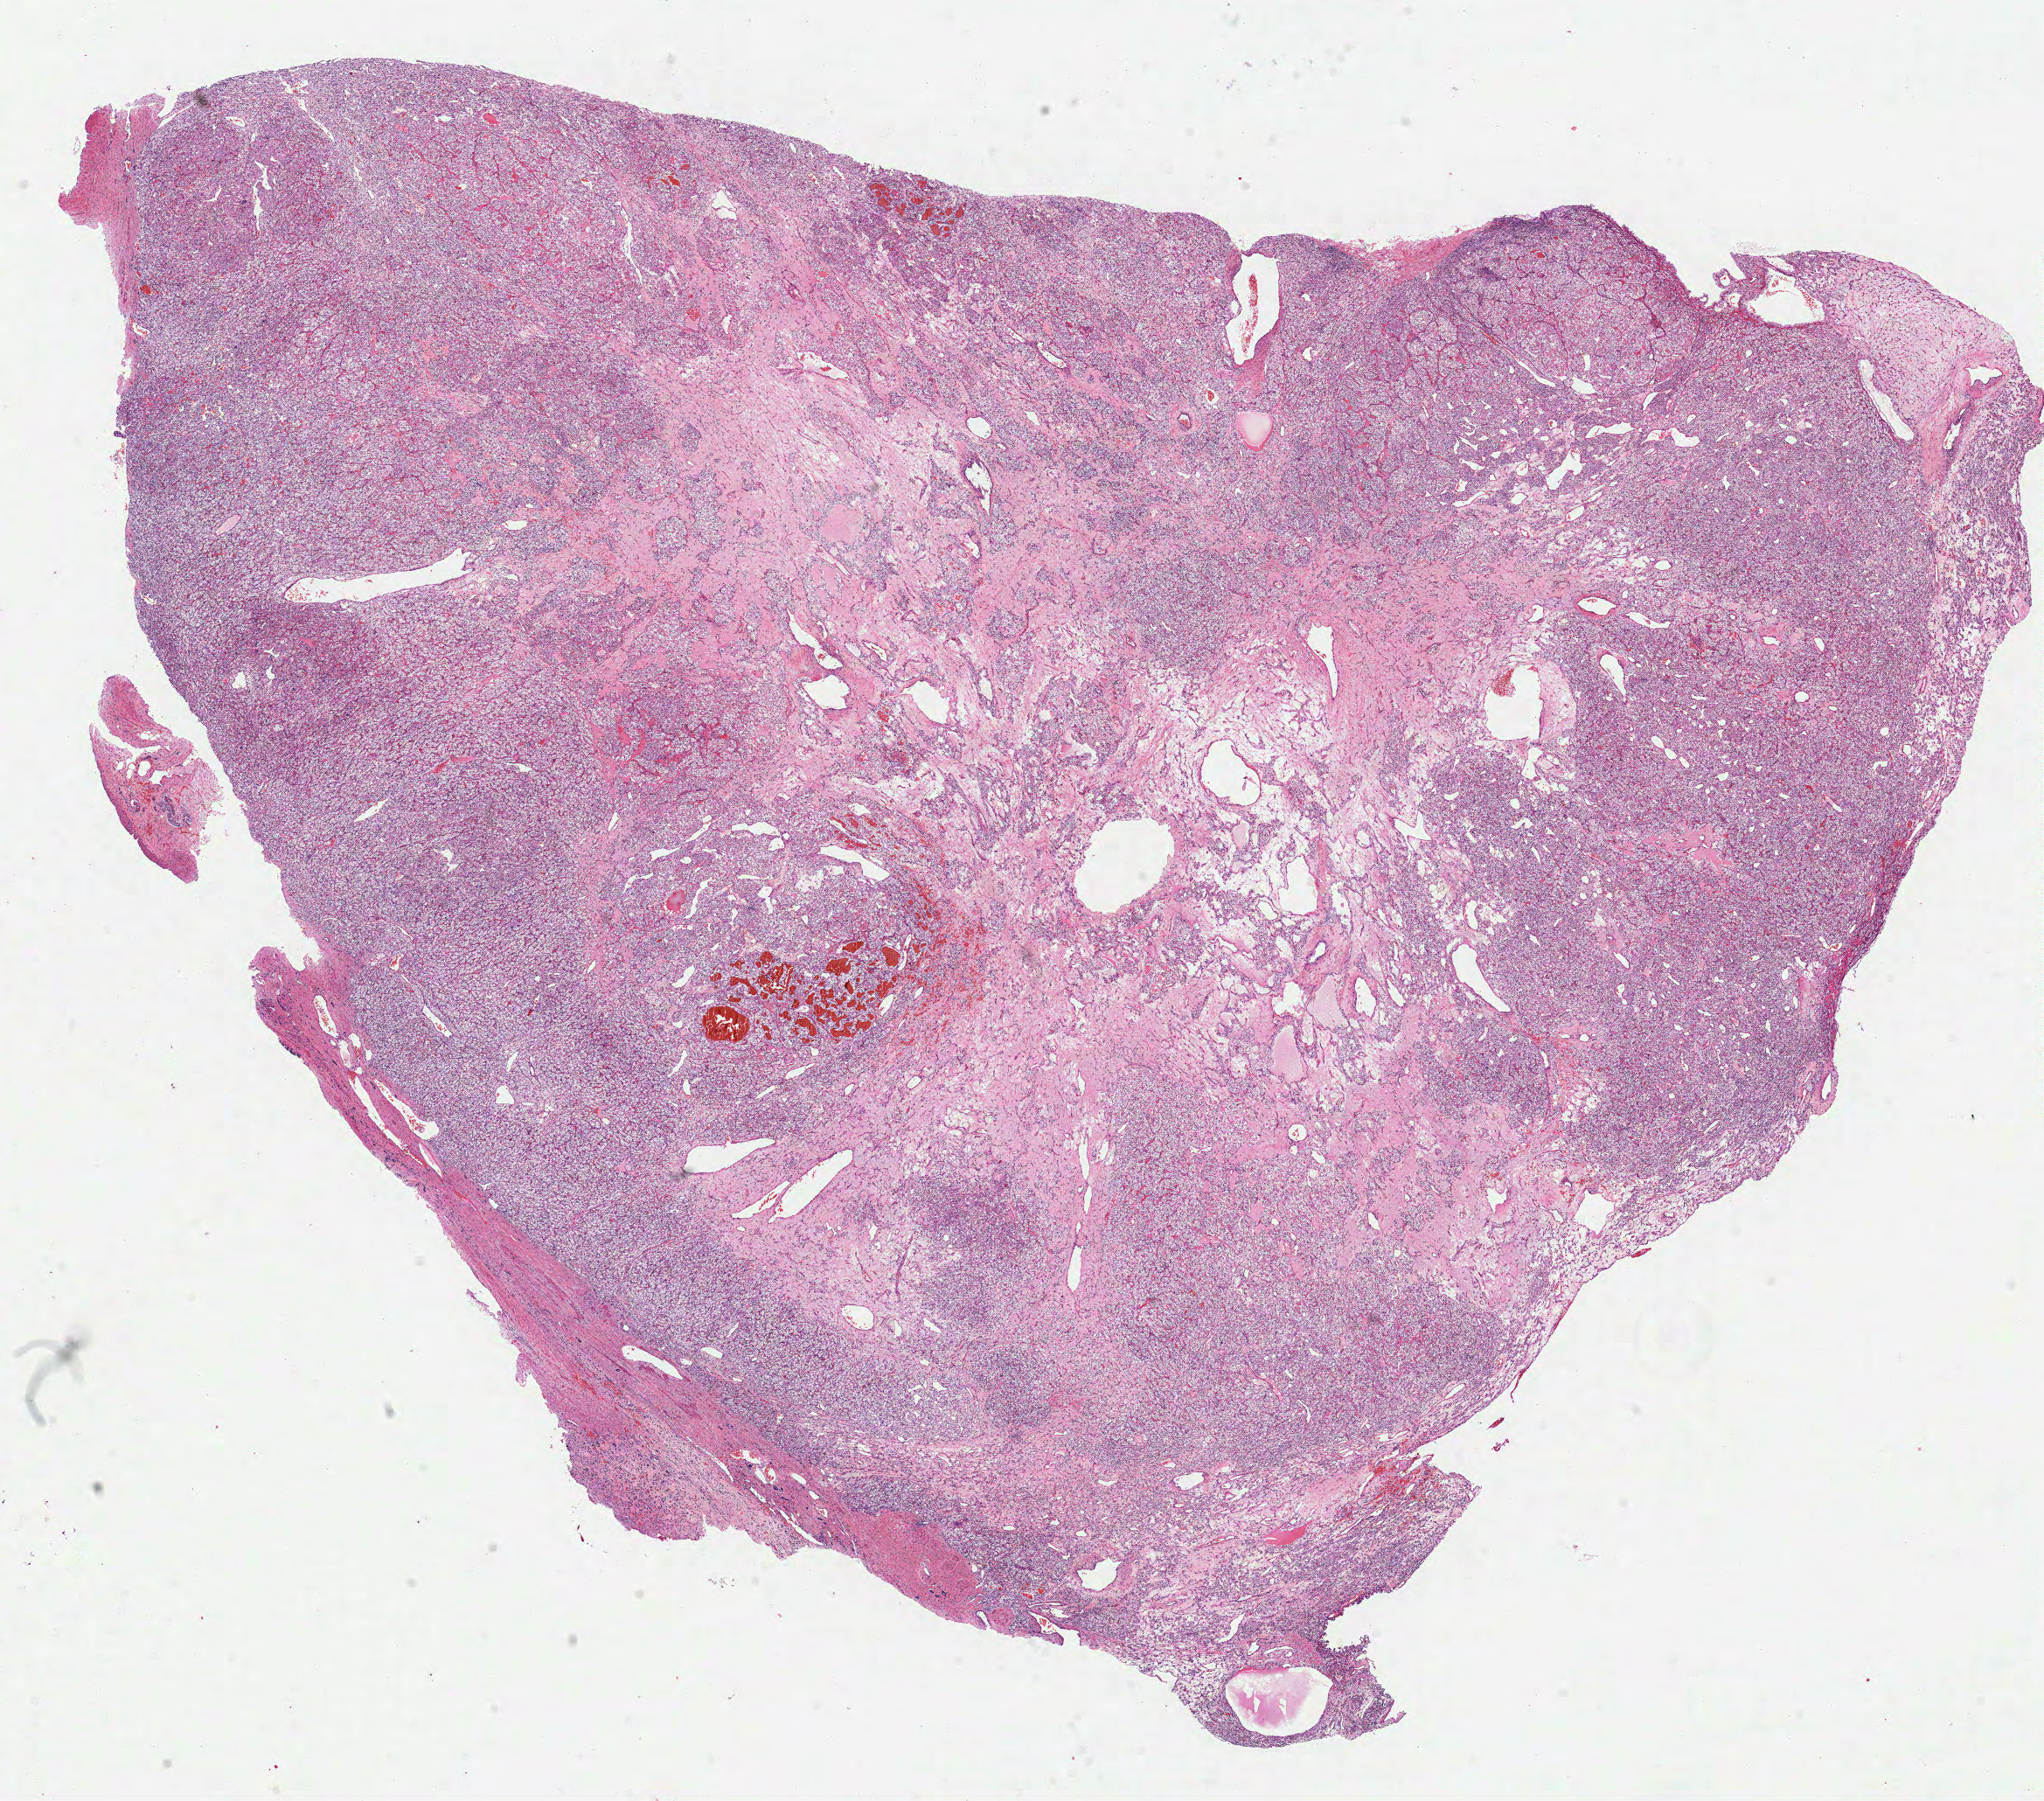
H&E-stained whole-slide image — shown as a low-resolution overview of the whole scanned area (about 18.9 x 16.6 mm, slide scanned at 40x). Formalin-fixed paraffin-embedded (FFPE) diagnostic section. Sample: primary tumour, kidney. Male, age 59 years at initial diagnosis.
Histologic diagnosis: Clear cell adenocarcinoma, NOS.